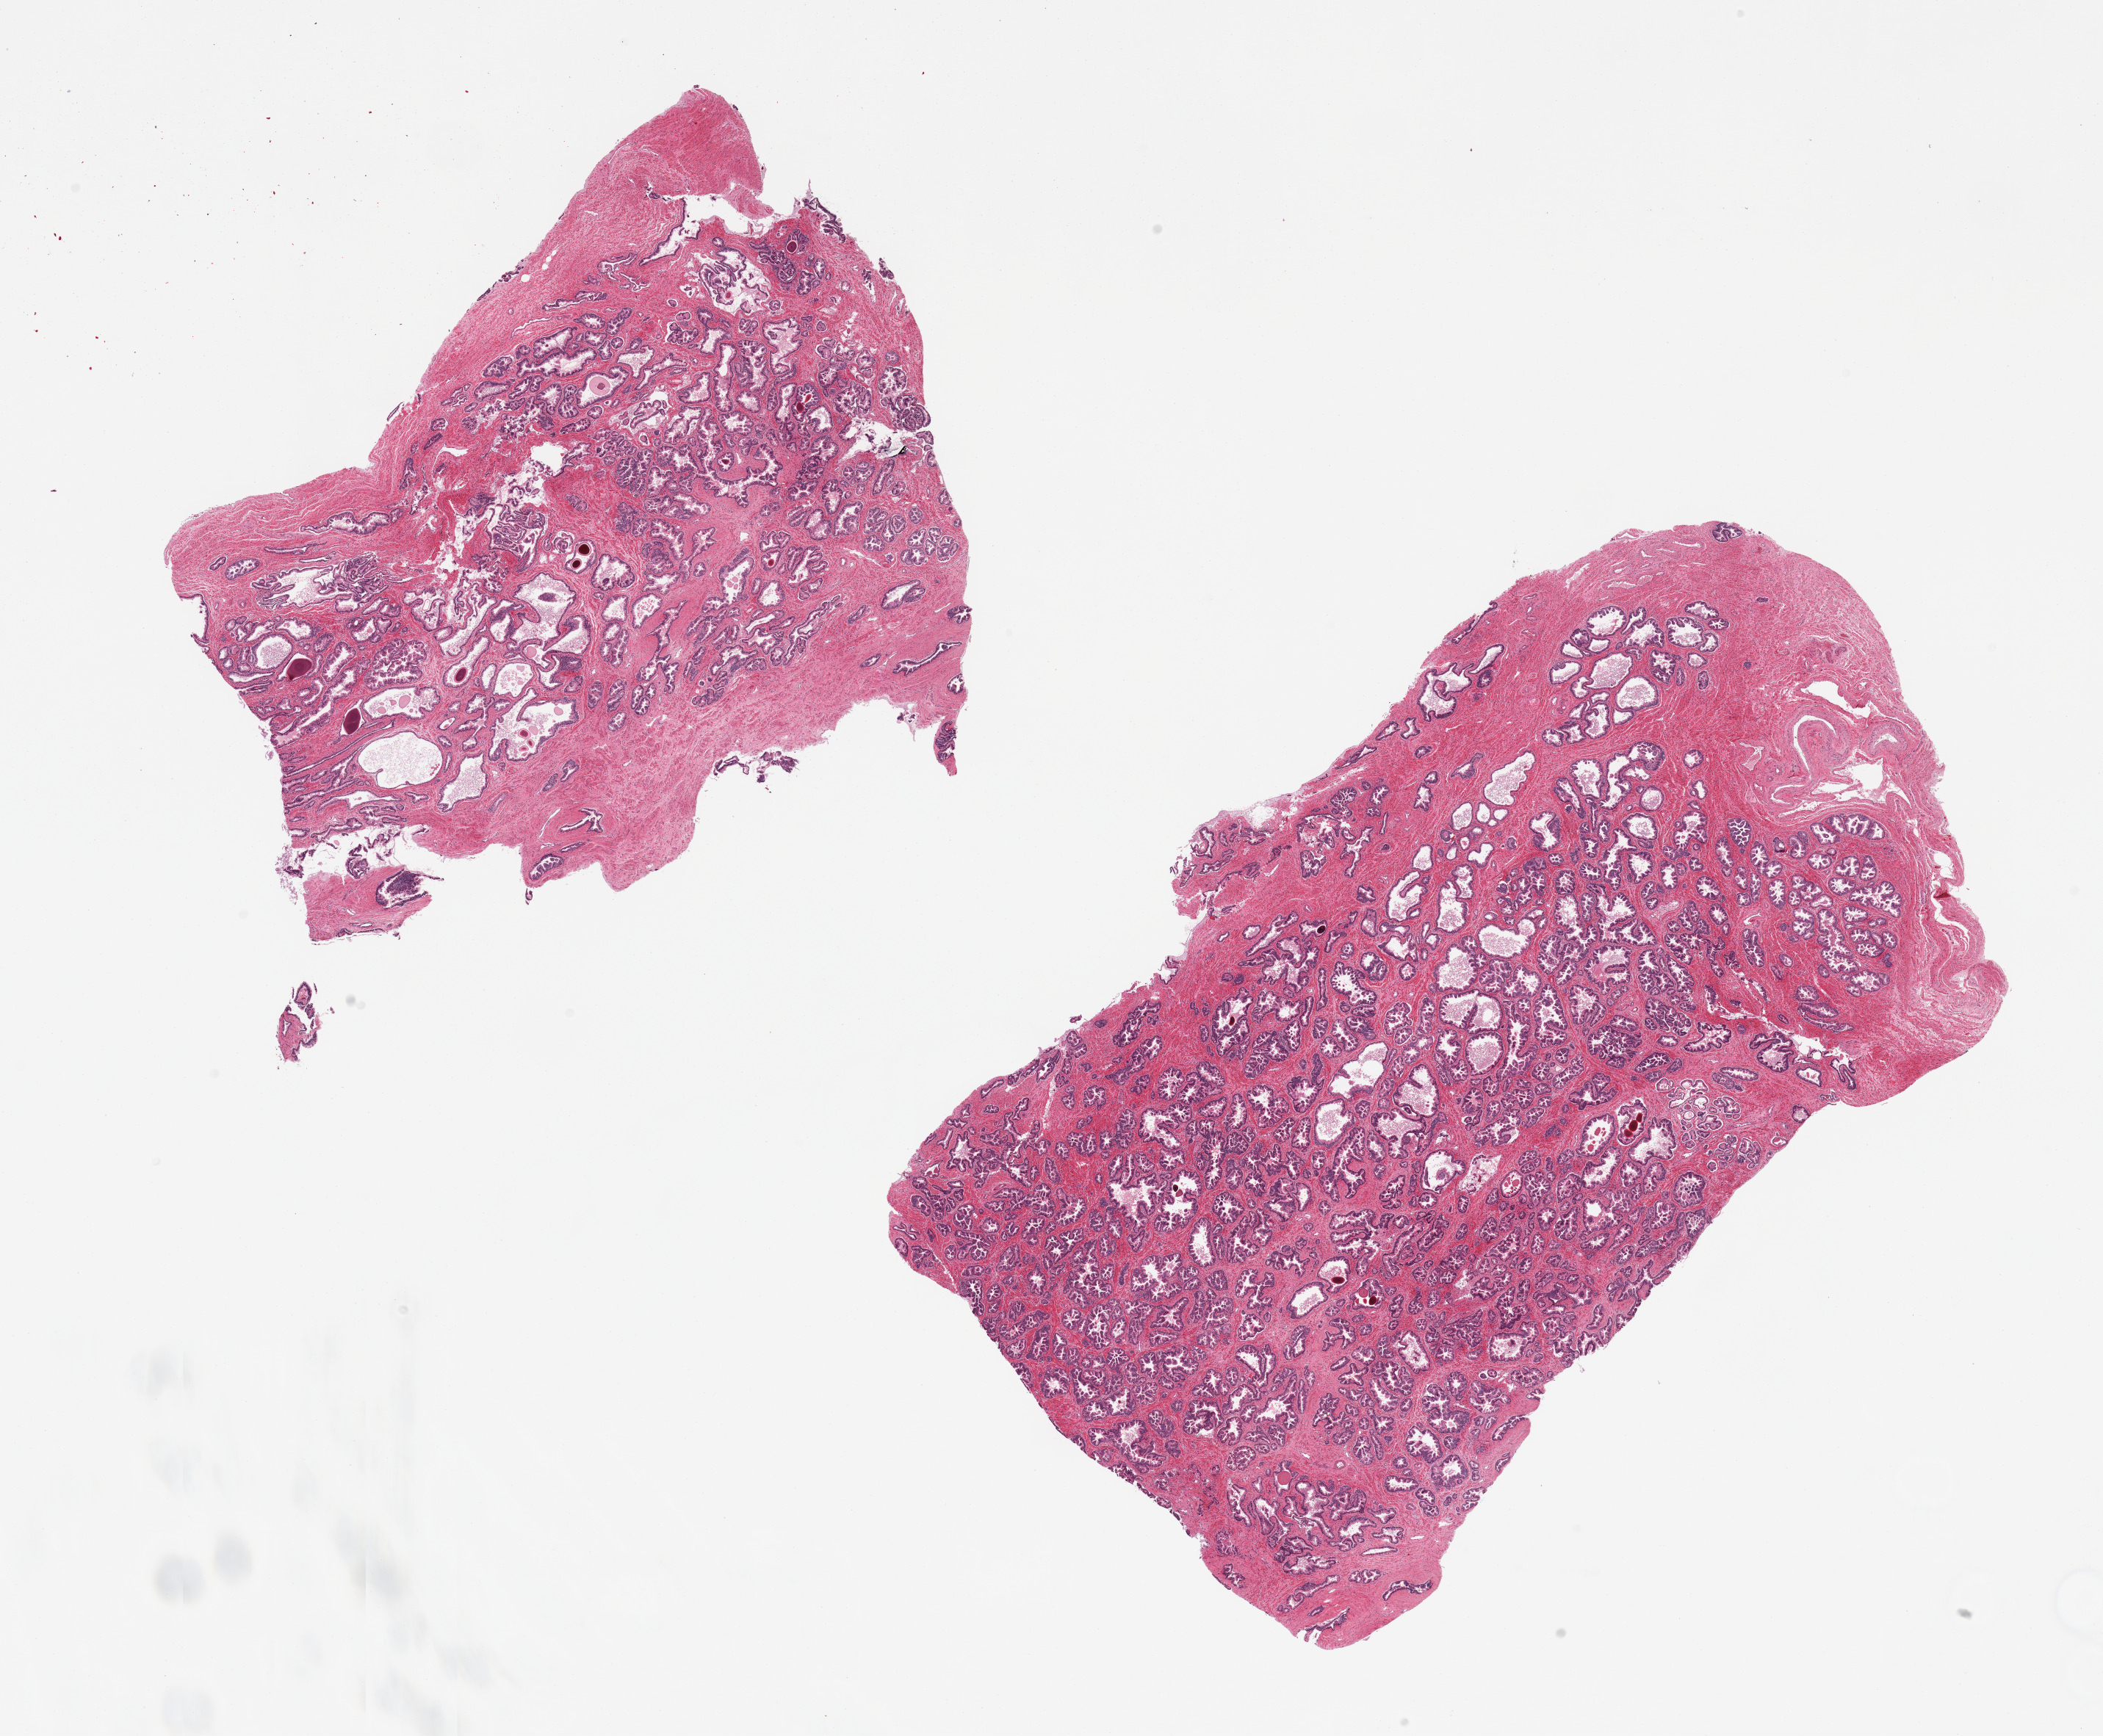
Digitized hematoxylin and eosin (H&E)-stained section — whole scanned area (about 22.6 x 18.7 mm) shown as a low-resolution overview, PAXgene-fixed, paraffin-embedded tissue, sampled site (target tissue): prostate, tissue donor sample. Male donor.
• reviewer comment on this tissue sample: 2 pieces; admixed glands and stroma